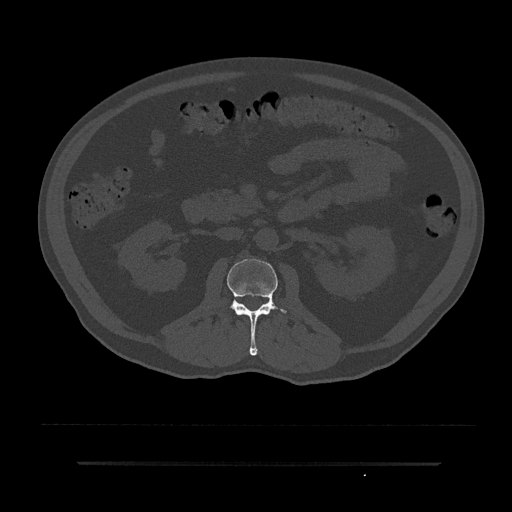
CT including the spine, one axial slice; slice 71 of 797 in the series (ordered by position); 120 kVp; bone window (W 1800 / L 400 HU); 512 × 512 image matrix, field of view 464 × 464 mm. Male patient, age 59 years. Case-level facts recorded for this patient, not image findings: primary cancer: bile ducts.
Outlined on this slice (semi-automatic segmentation, software-assisted and operator-edited):
- L2 vertebra: box from (x=227, y=259) to (x=287, y=356) px